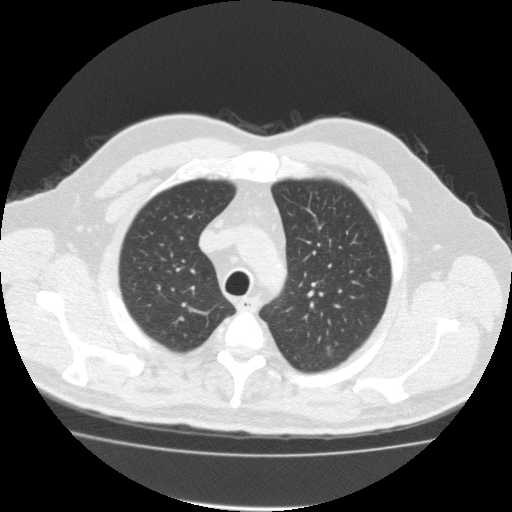
Low-dose screening chest CT, one axial slice; 120 kVp; lung window (W 1500 / L -600 HU); 512 × 512 image matrix.
Outlined on this slice (outlined manually by an expert reader):
- lesion 1 (tumor, upper lobe of left lung): bounding box (x1, y1, x2, y2) in pixels: (327, 344, 335, 358)